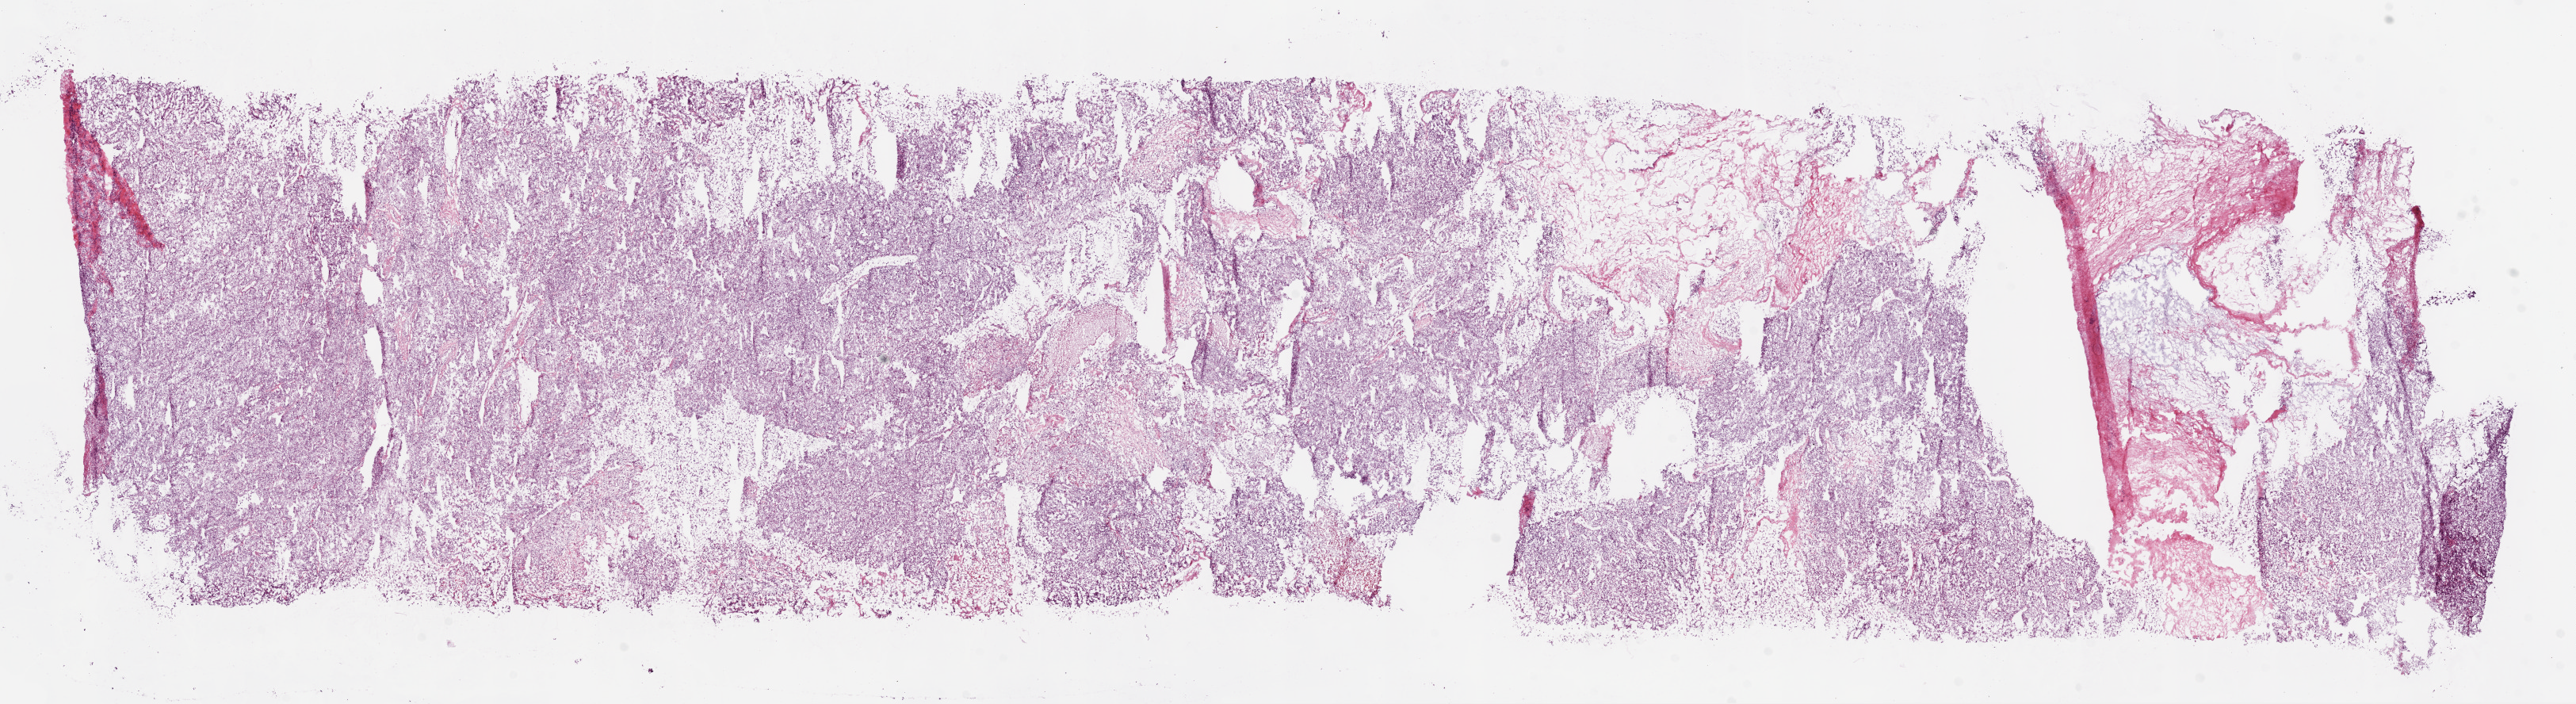
Digitized H&E tissue section (whole slide), low-resolution overview of the scanned area, about 26.1 x 7.1 mm (from a 20x scan). Frozen section from the top of the tissue portion. Primary tumour sample from the kidney. Patient: female, age at initial diagnosis 72 years. Histologic grade: G3 (poorly differentiated). Composition of this section per pathologist review: tumour cells 80%, tumour nuclei 90%, normal cells 0%, stromal cells 20%, necrosis 0%.
AJCC pathologic stage: III. Histologic diagnosis: Clear cell adenocarcinoma, NOS.